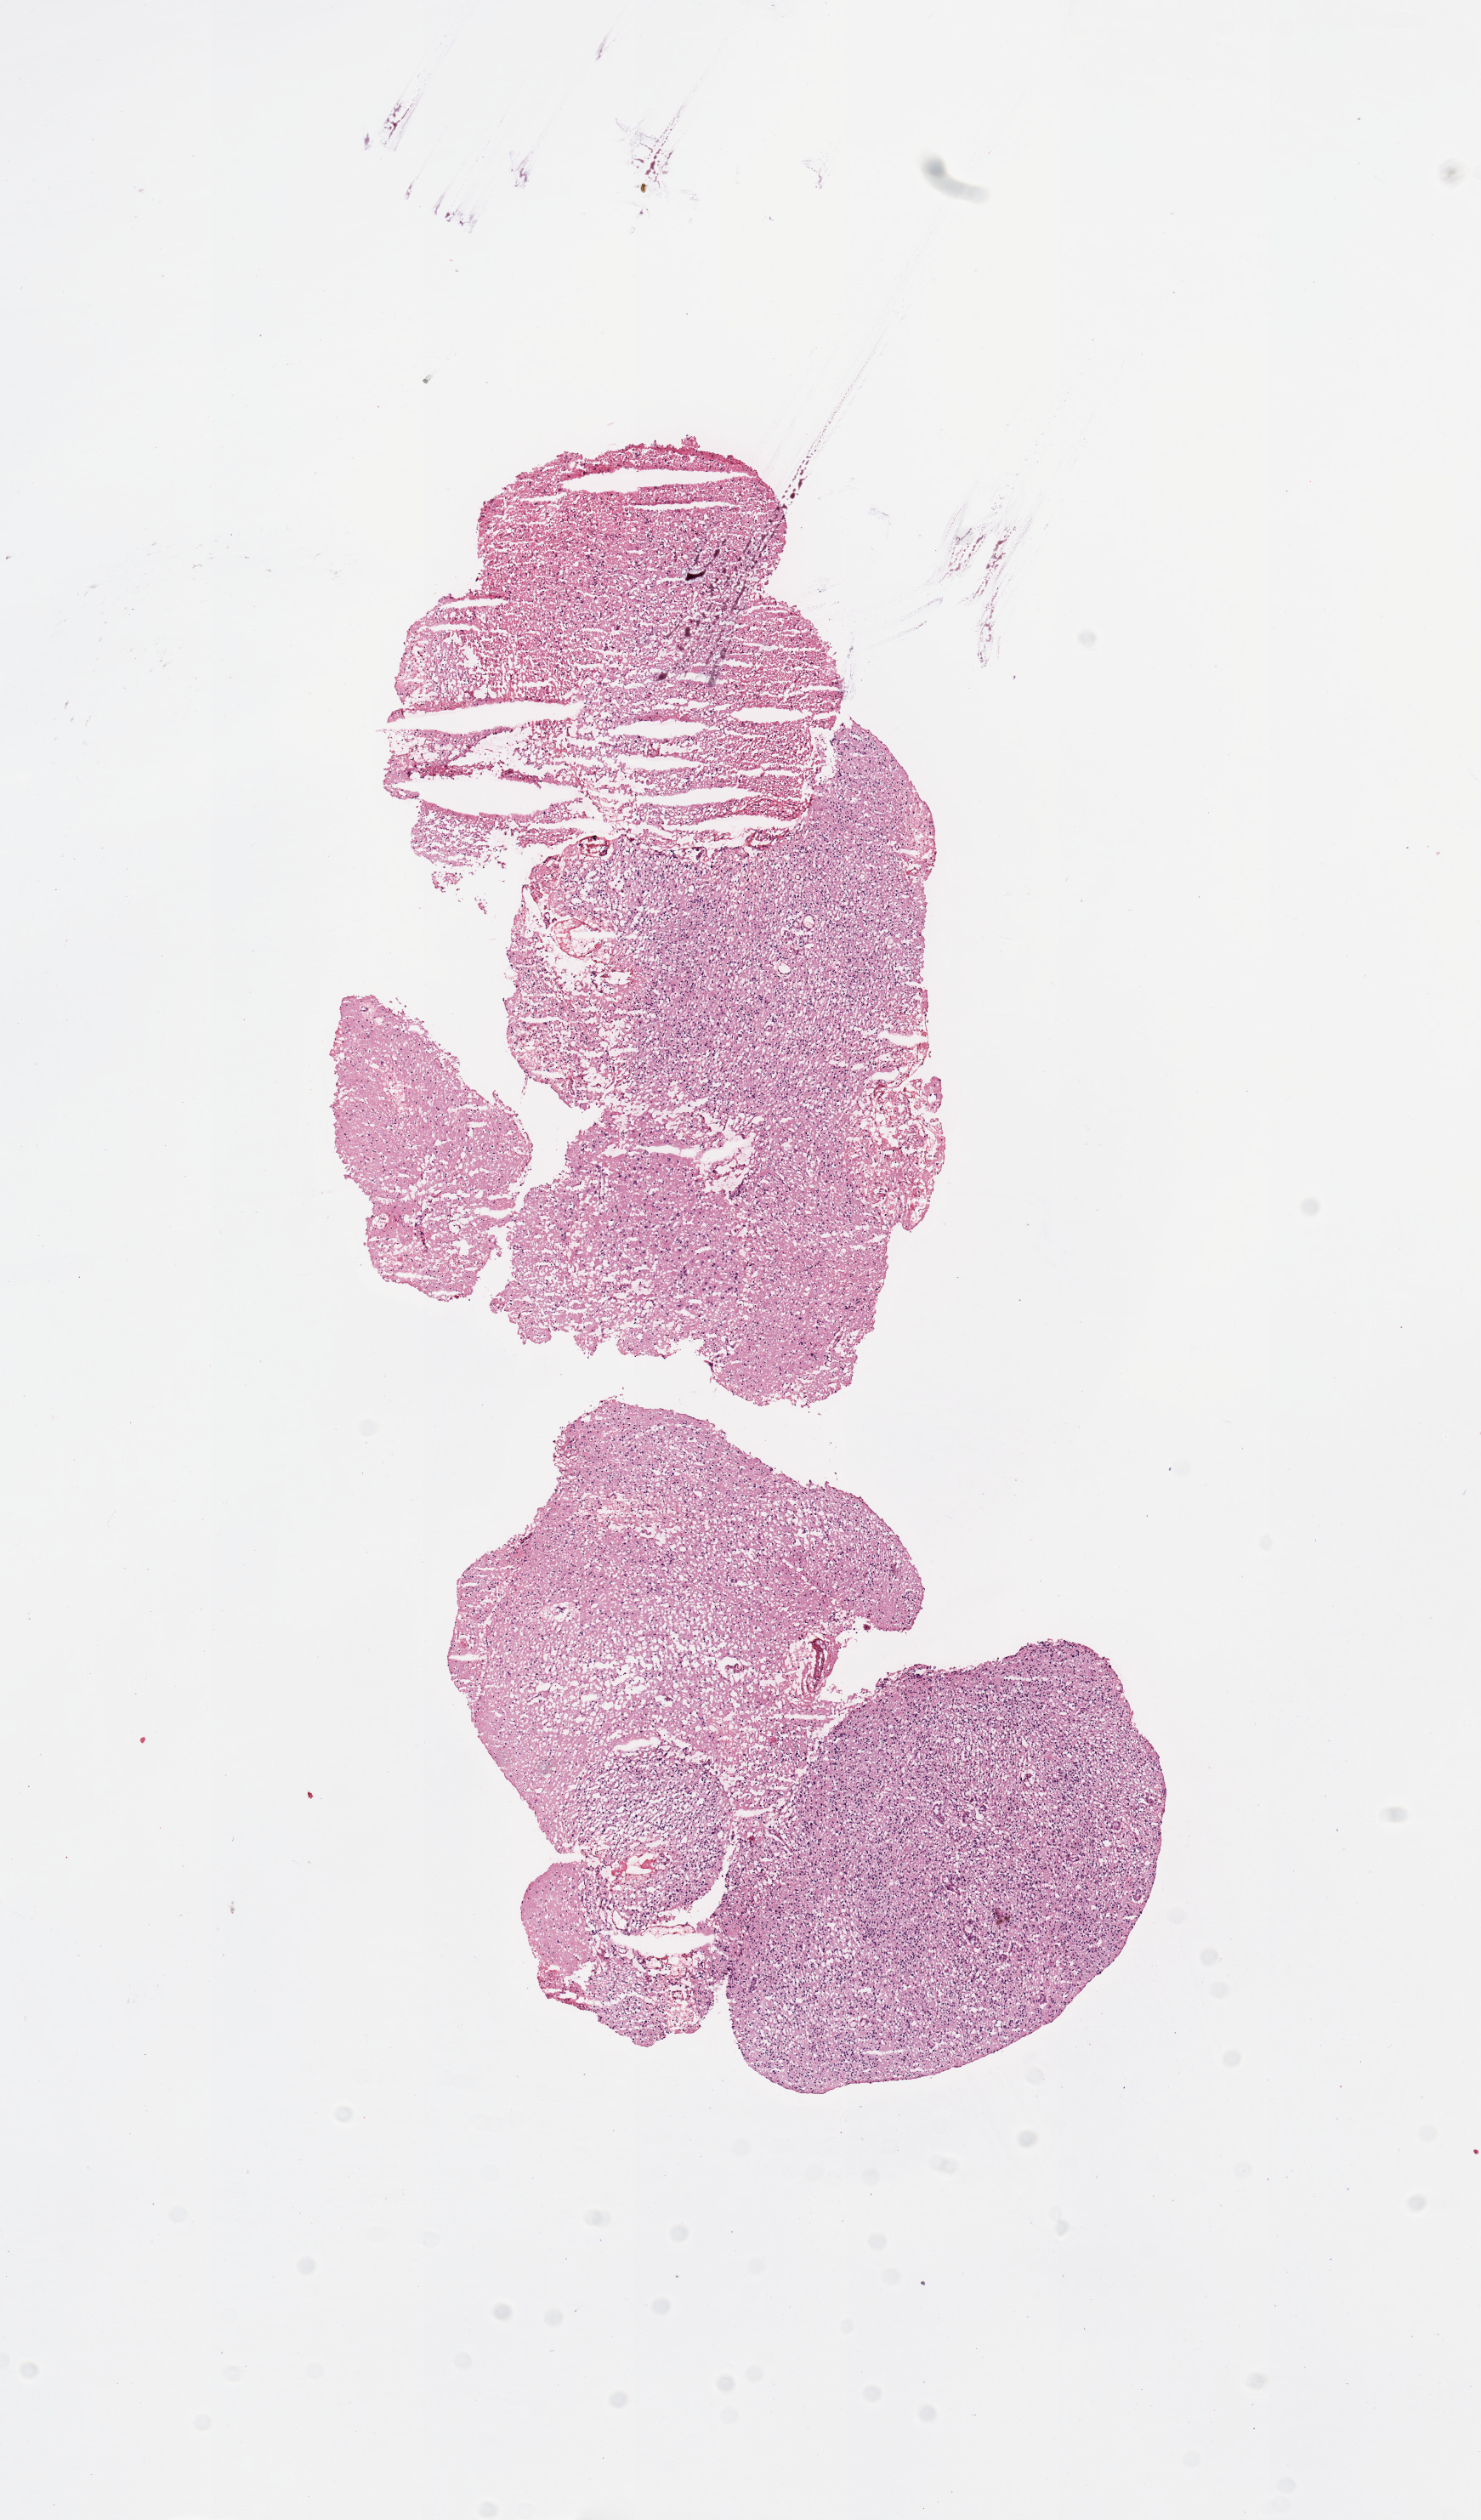
H&E whole-slide image — a low-resolution overview of the entire scanned area, about 6.9 x 11.7 mm (acquisition: 20x scan). Brain, tumour tissue. Male, 62 y/o.
Patient diagnosis (cohort enrolment): glioblastoma multiforme (brain).